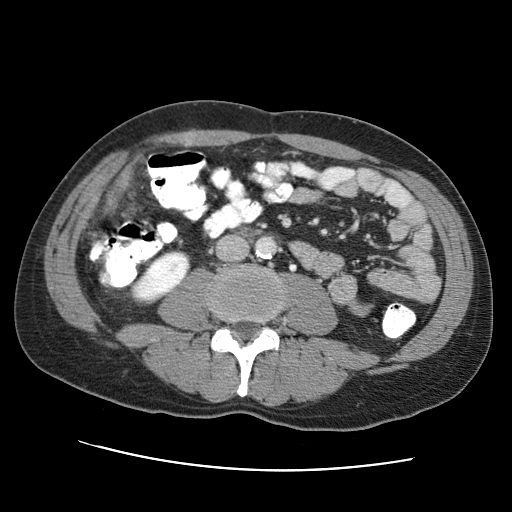
Contrast-enhanced abdominal CT (liver protocol), one axial slice. Position 4 of 95 along the scan axis. 120 kVp. One of 2 acquisitions stored at this slice position. Soft-tissue window (W 400 / L 40 HU). 2.5 mm slice thickness. 512 × 512 image matrix. From the clinical record (not read from this slice): diagnosis: hepatocellular carcinoma (patient treated with transarterial chemoembolisation; whether this scan precedes or follows treatment is not stated here); TNM stage (as recorded): Stage-IVA; Child-Pugh class: A; tumour differentiation: moderately differentiated; tumour nodularity: multinodular.
Structures marked on this image (semi-automatically segmented with operator editing):
- liver parenchyma outside the tumour (the mass and vessels are separate outlines, so this box may not span the whole liver): bounding box (x1, y1, x2, y2) in pixels: (108, 168, 130, 203)